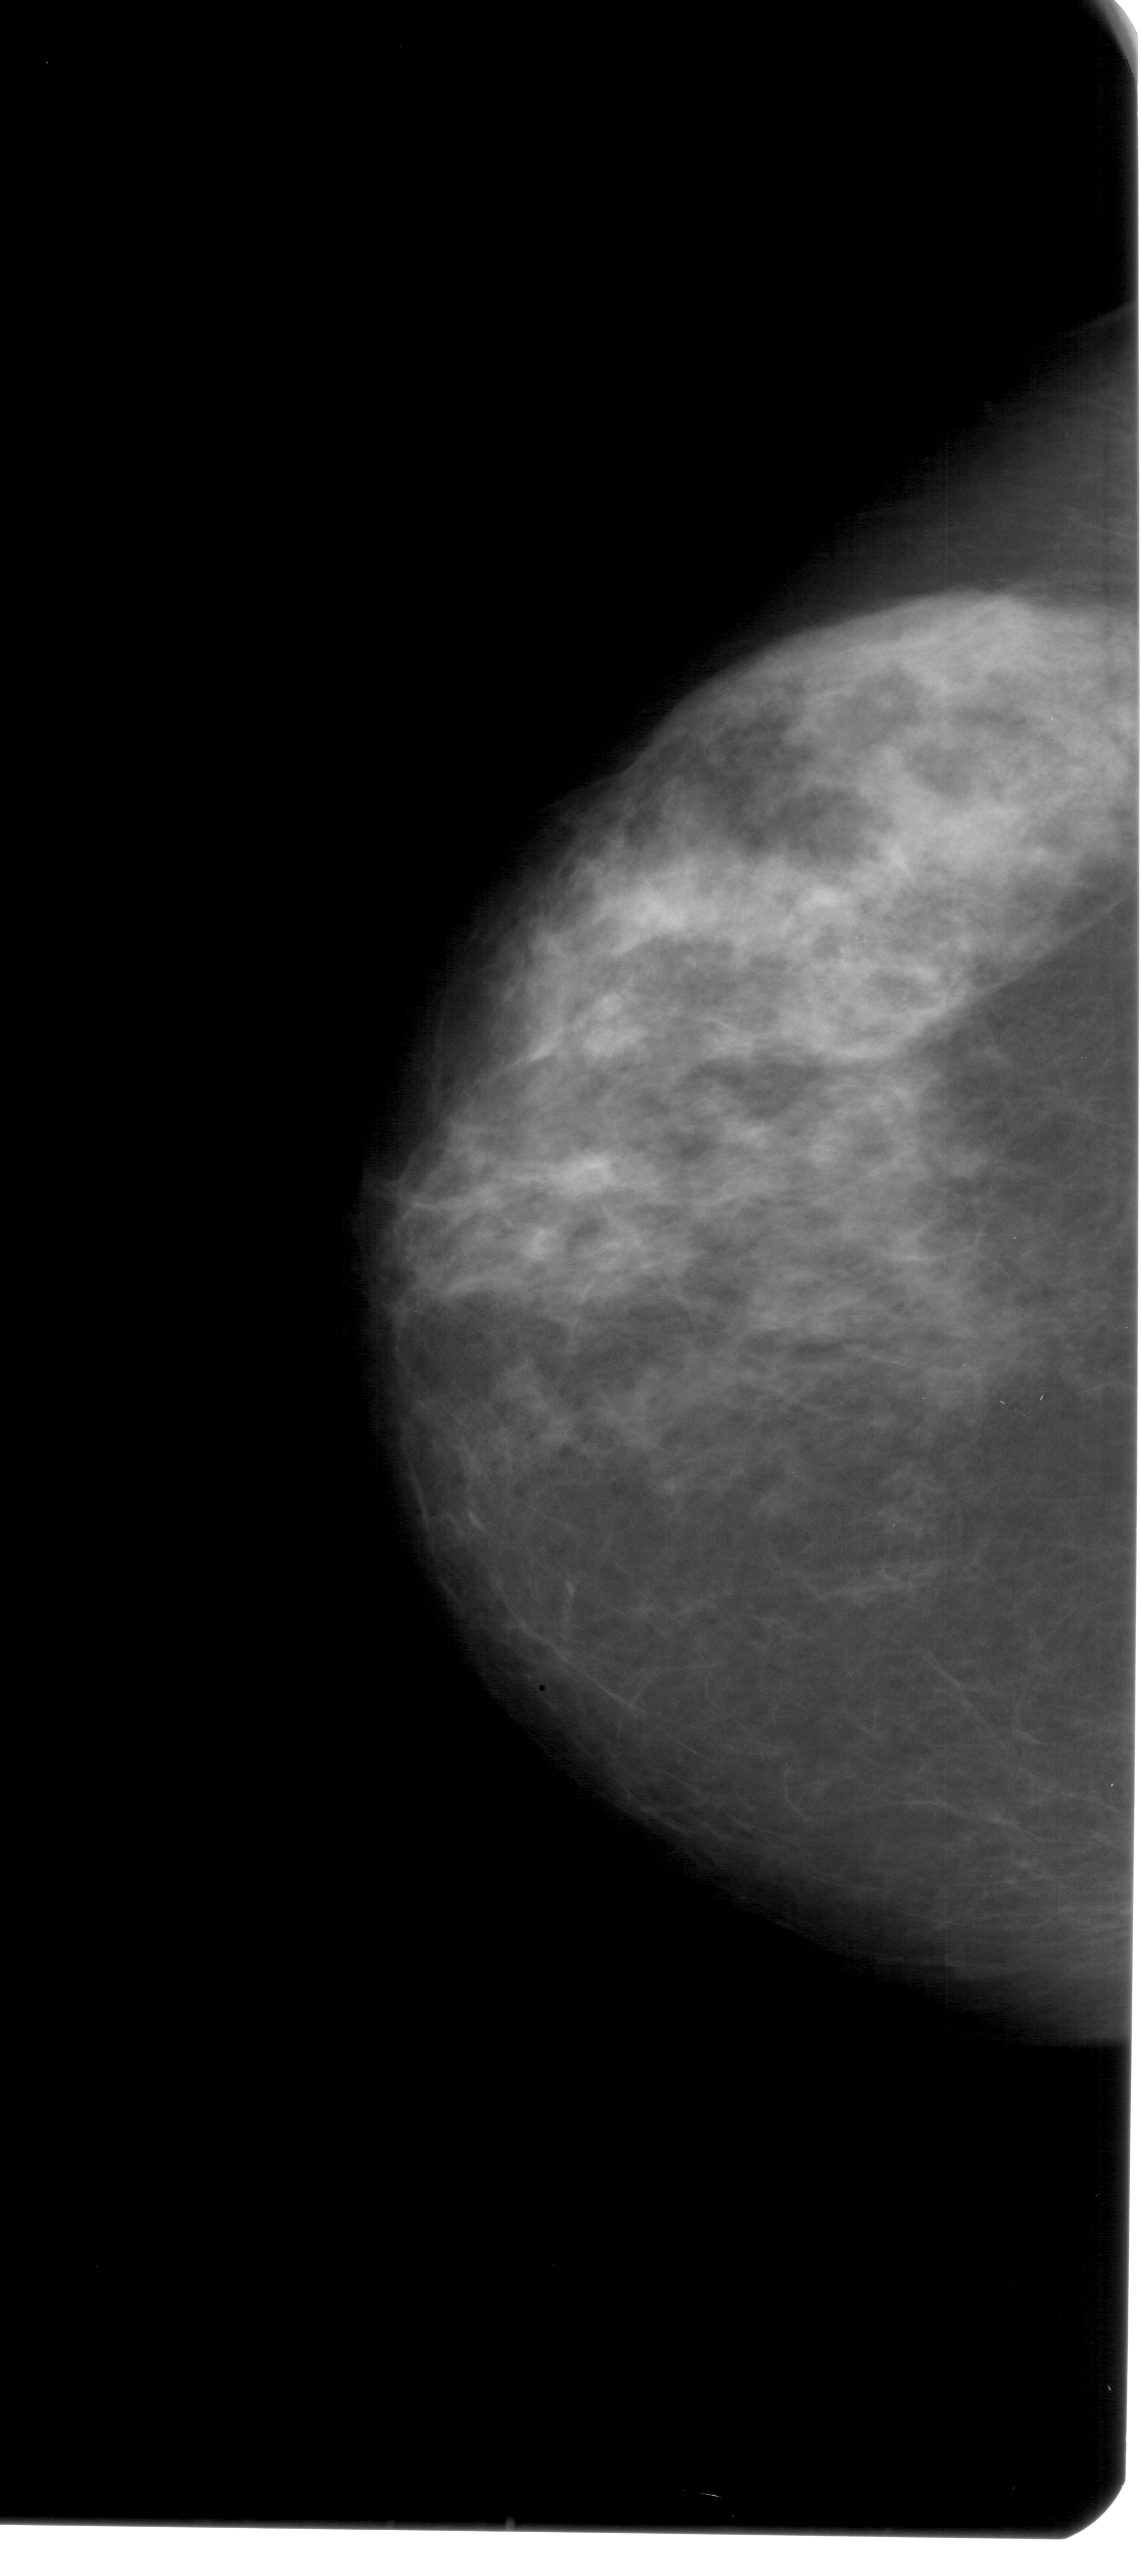
Scanned film-screen mammogram; left breast; craniocaudal (CC) view; breast composition: heterogeneously dense (BI-RADS density category 3 of 4).
Radiologist-marked abnormalities on this image: calcifications, morphology pleomorphic, distribution clustered; BI-RADS assessment category 4; subtlety rating 2 on a 1 (subtle) to 5 (obvious) scale; pathology (as recorded): benign.